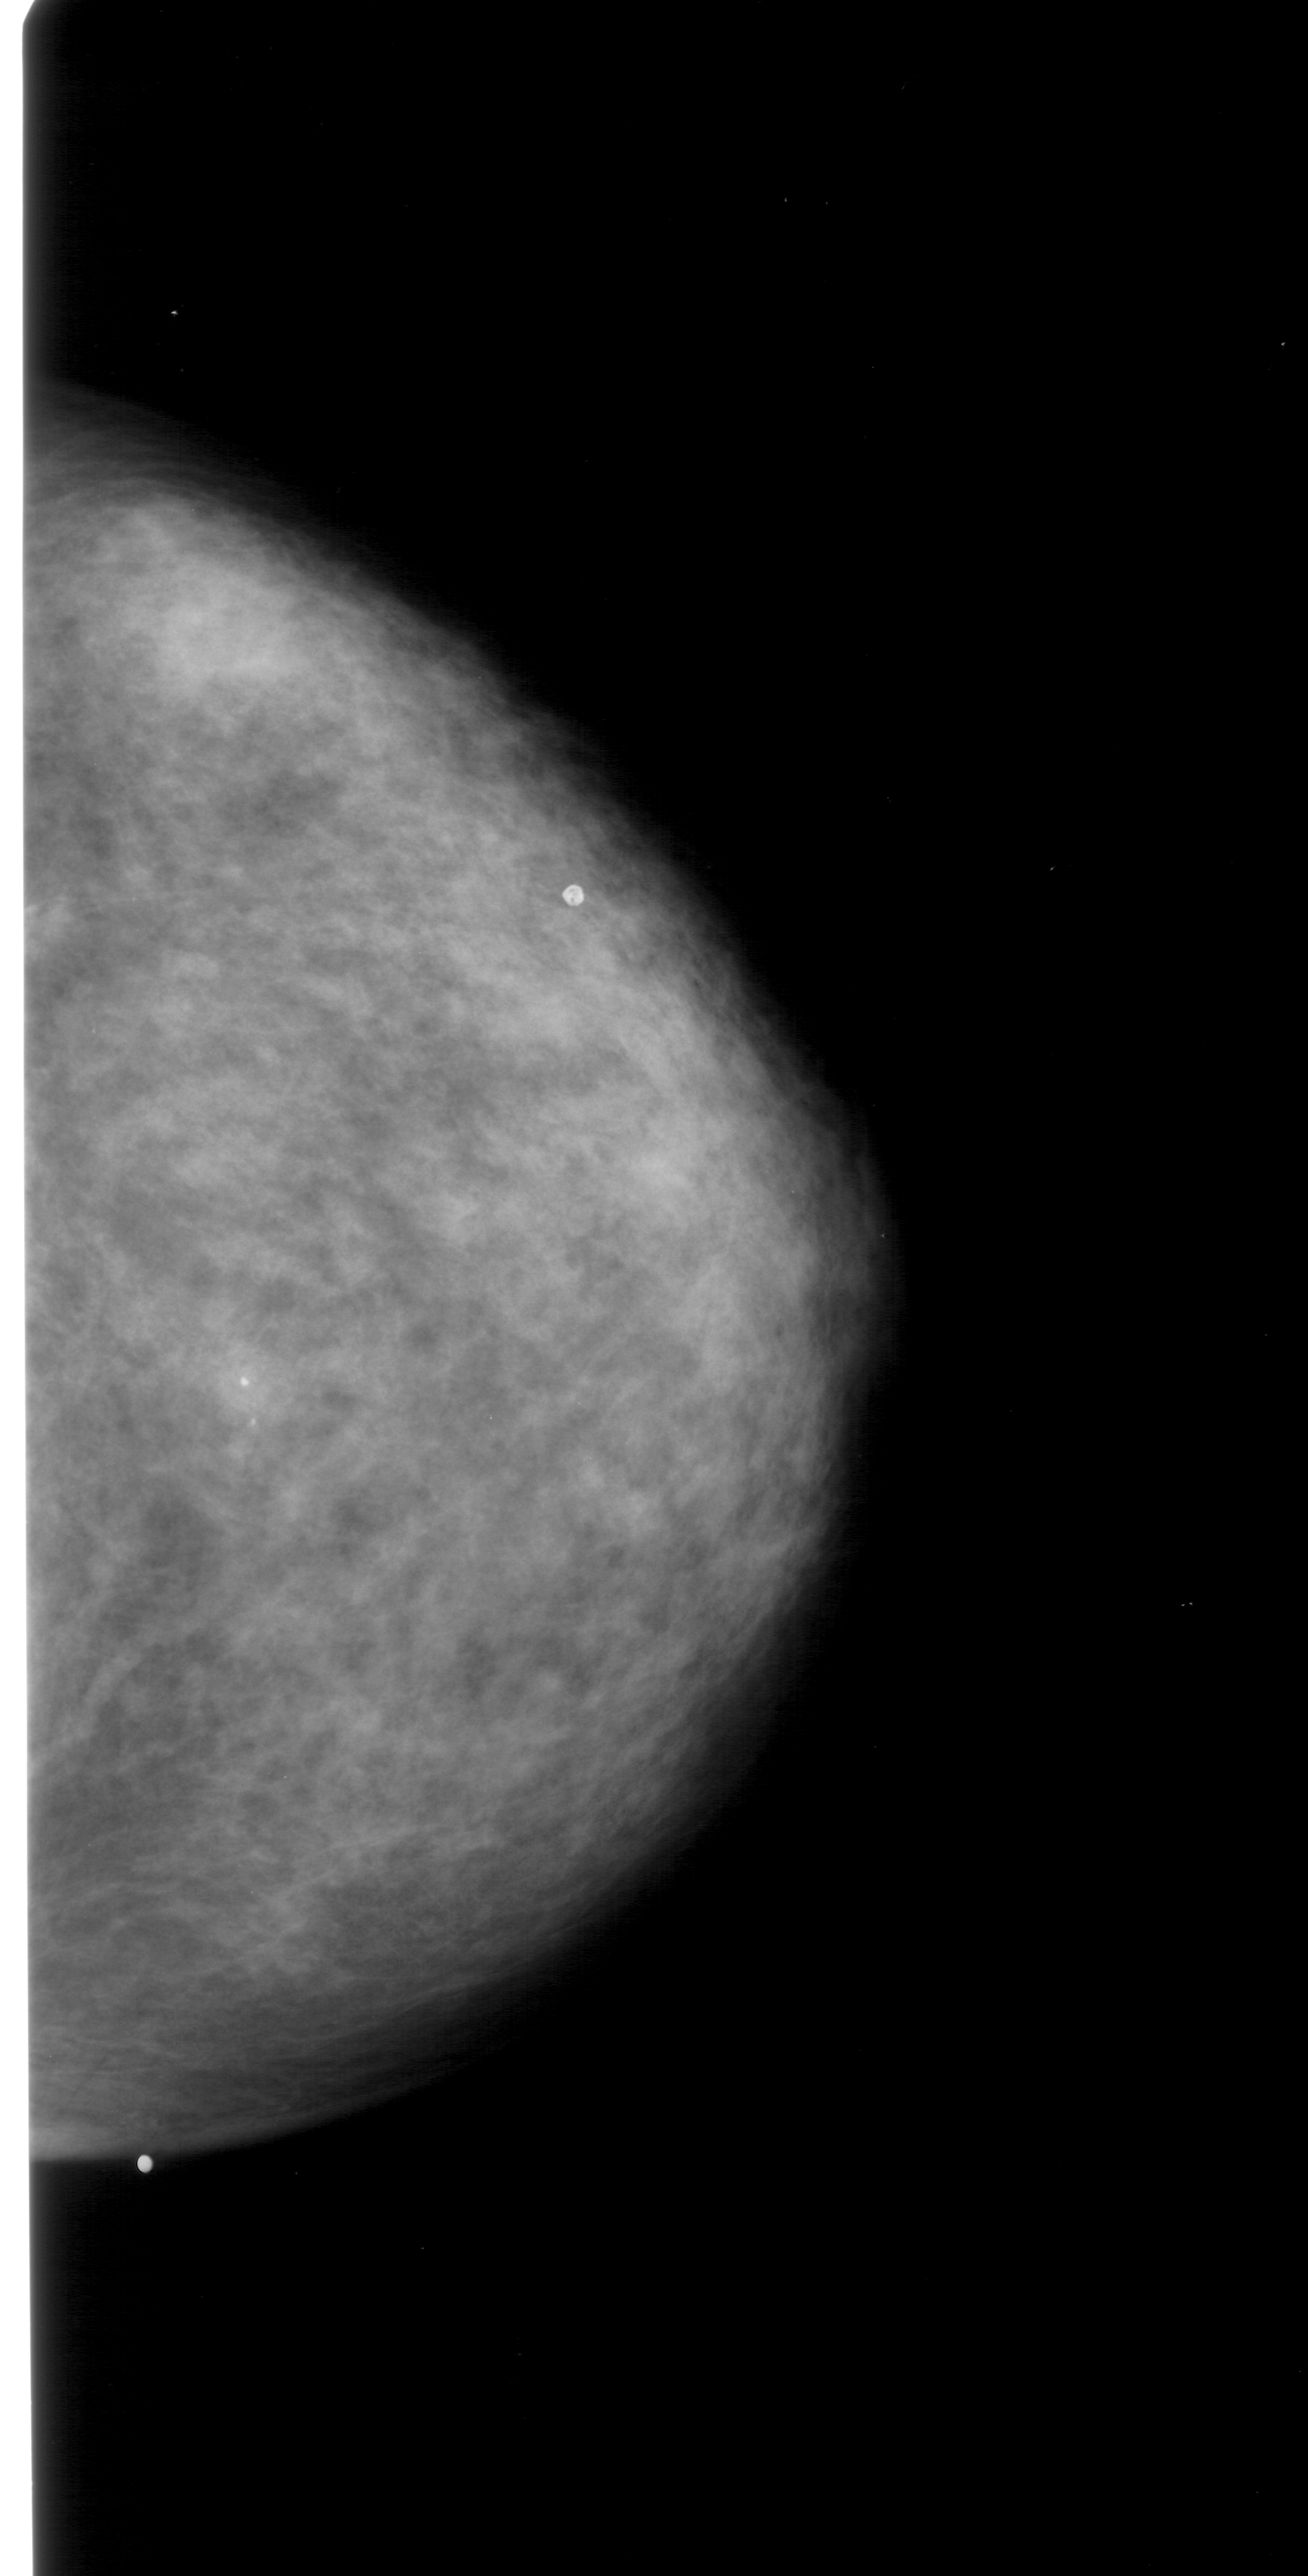
Scanned film-screen mammogram, right breast, craniocaudal (CC) view, BI-RADS breast density category 3 (scale 1–4).
- Finding: calcifications, morphology pleomorphic, distribution clustered; BI-RADS assessment category 4; subtlety rating 2 on a 1 (subtle) to 5 (obvious) scale; pathology result (as recorded, not read from the image): malignant.